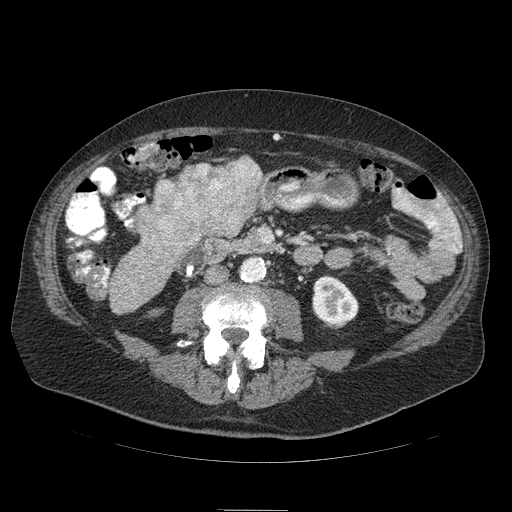
Contrast-enhanced abdominal CT (liver protocol), one axial slice; position 16 of 103 along the scan axis; reconstruction kernel STANDARD; soft-tissue window (W 400 / L 40 HU); 2.5 mm slice thickness; 512 × 512 image matrix, field of view 440 × 440 mm. Case-level facts recorded for this patient, not image findings: diagnosis: hepatocellular carcinoma (patient treated with transarterial chemoembolisation; whether this scan precedes or follows treatment is not stated here); TNM stage (as recorded): Stage-IIIA; Child-Pugh class: B.
Outlined on this slice (semi-automatic segmentation, software-assisted and operator-edited):
- liver parenchyma outside the tumour (the mass and vessels are separate outlines, so this box may not span the whole liver): bounding box [x1, y1, x2, y2] px = [262, 187, 264, 191]
- mass: [134, 158, 265, 262]